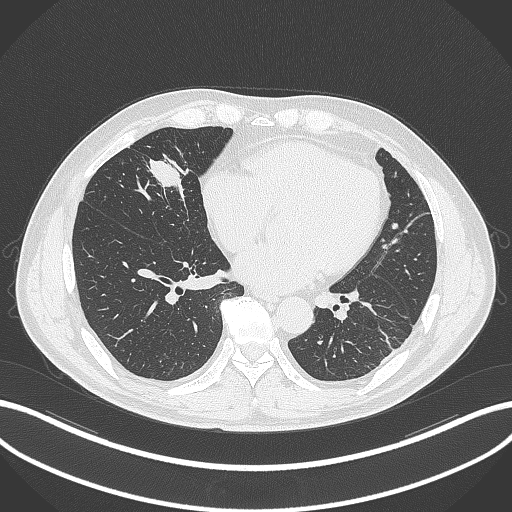
Chest CT, one axial slice. Position 106 of 399 along the scan axis. 120 kVp. Lung window (W 1500 / L -600 HU). 512 × 512 image matrix, field of view 400 × 400 mm. Male patient, age 59 years. Case-level facts recorded for this patient, not image findings: clinical TNM (as recorded): T2a N1 M0.
Outlined on this slice (bounding box drawn by a radiologist):
- lung tumour (recorded histology: adenocarcinoma): bounding box <144,156,190,208> (left, top, right, bottom; pixels)